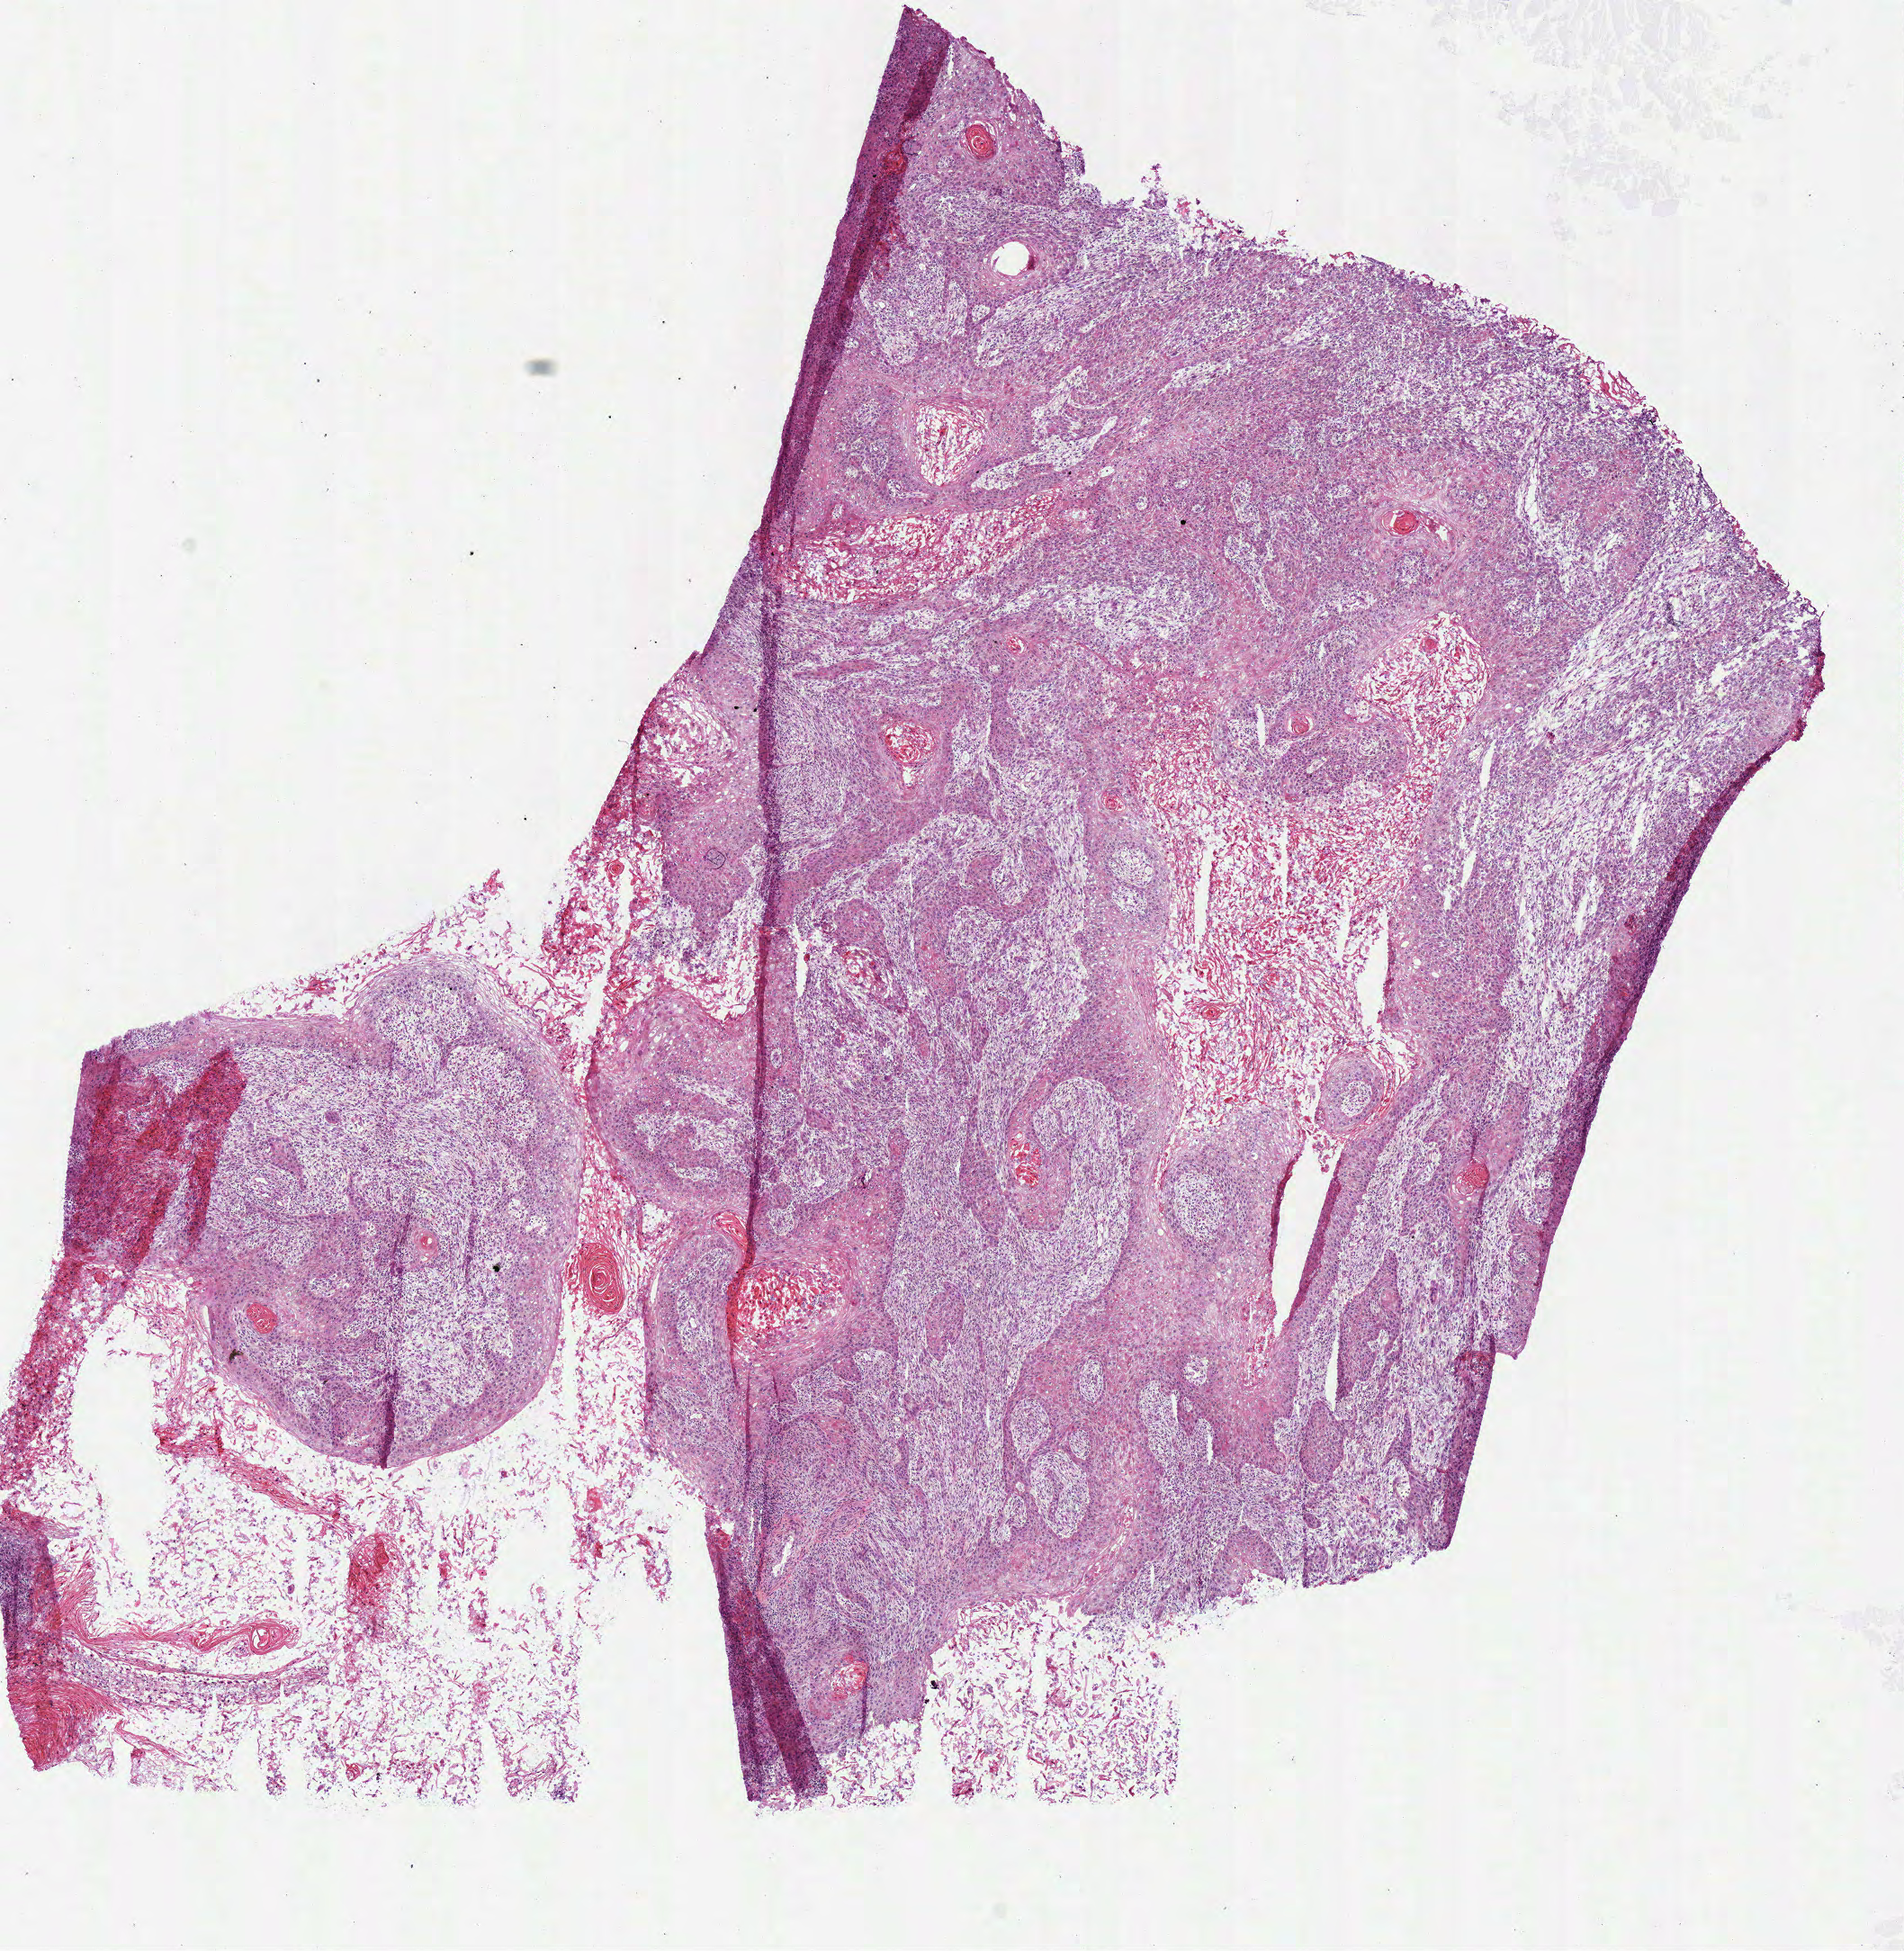
H&E-stained whole-slide image, shown as a low-resolution overview of the whole scanned area (about 8.3 x 8.5 mm), frozen section, lung, primary tumour sample. Male patient; age at initial diagnosis 85 years. Composition of this section per pathologist review: tumour cells 85%, tumour nuclei 71%.
Diagnosis: Squamous cell carcinoma, NOS (upper lobe, lung).